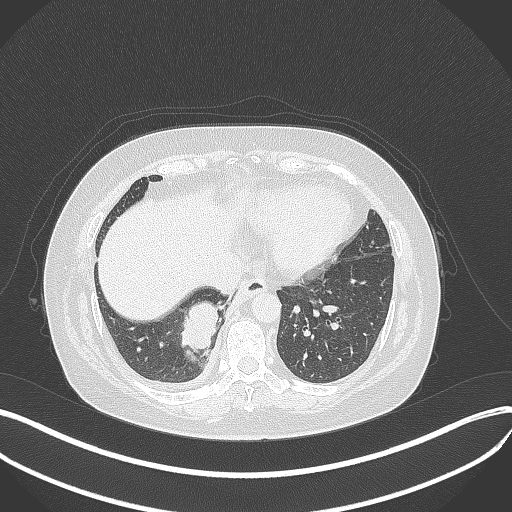
Chest CT, one axial slice; slice 104 of 381 in the series (ordered by position); 120 kVp; lung window (W 1500 / L -600 HU); 1 mm slice thickness; 512 × 512 image matrix. Female patient, age 56 years. Case-level facts recorded for this patient, not image findings: clinical TNM (as recorded): T2b N1 M0; histopathological grade: G3.
Outlined on this slice (bounding box drawn by a radiologist):
- lung tumour (recorded histology: small cell carcinoma): bounding box (x1, y1, x2, y2) in pixels: (180, 296, 225, 356)